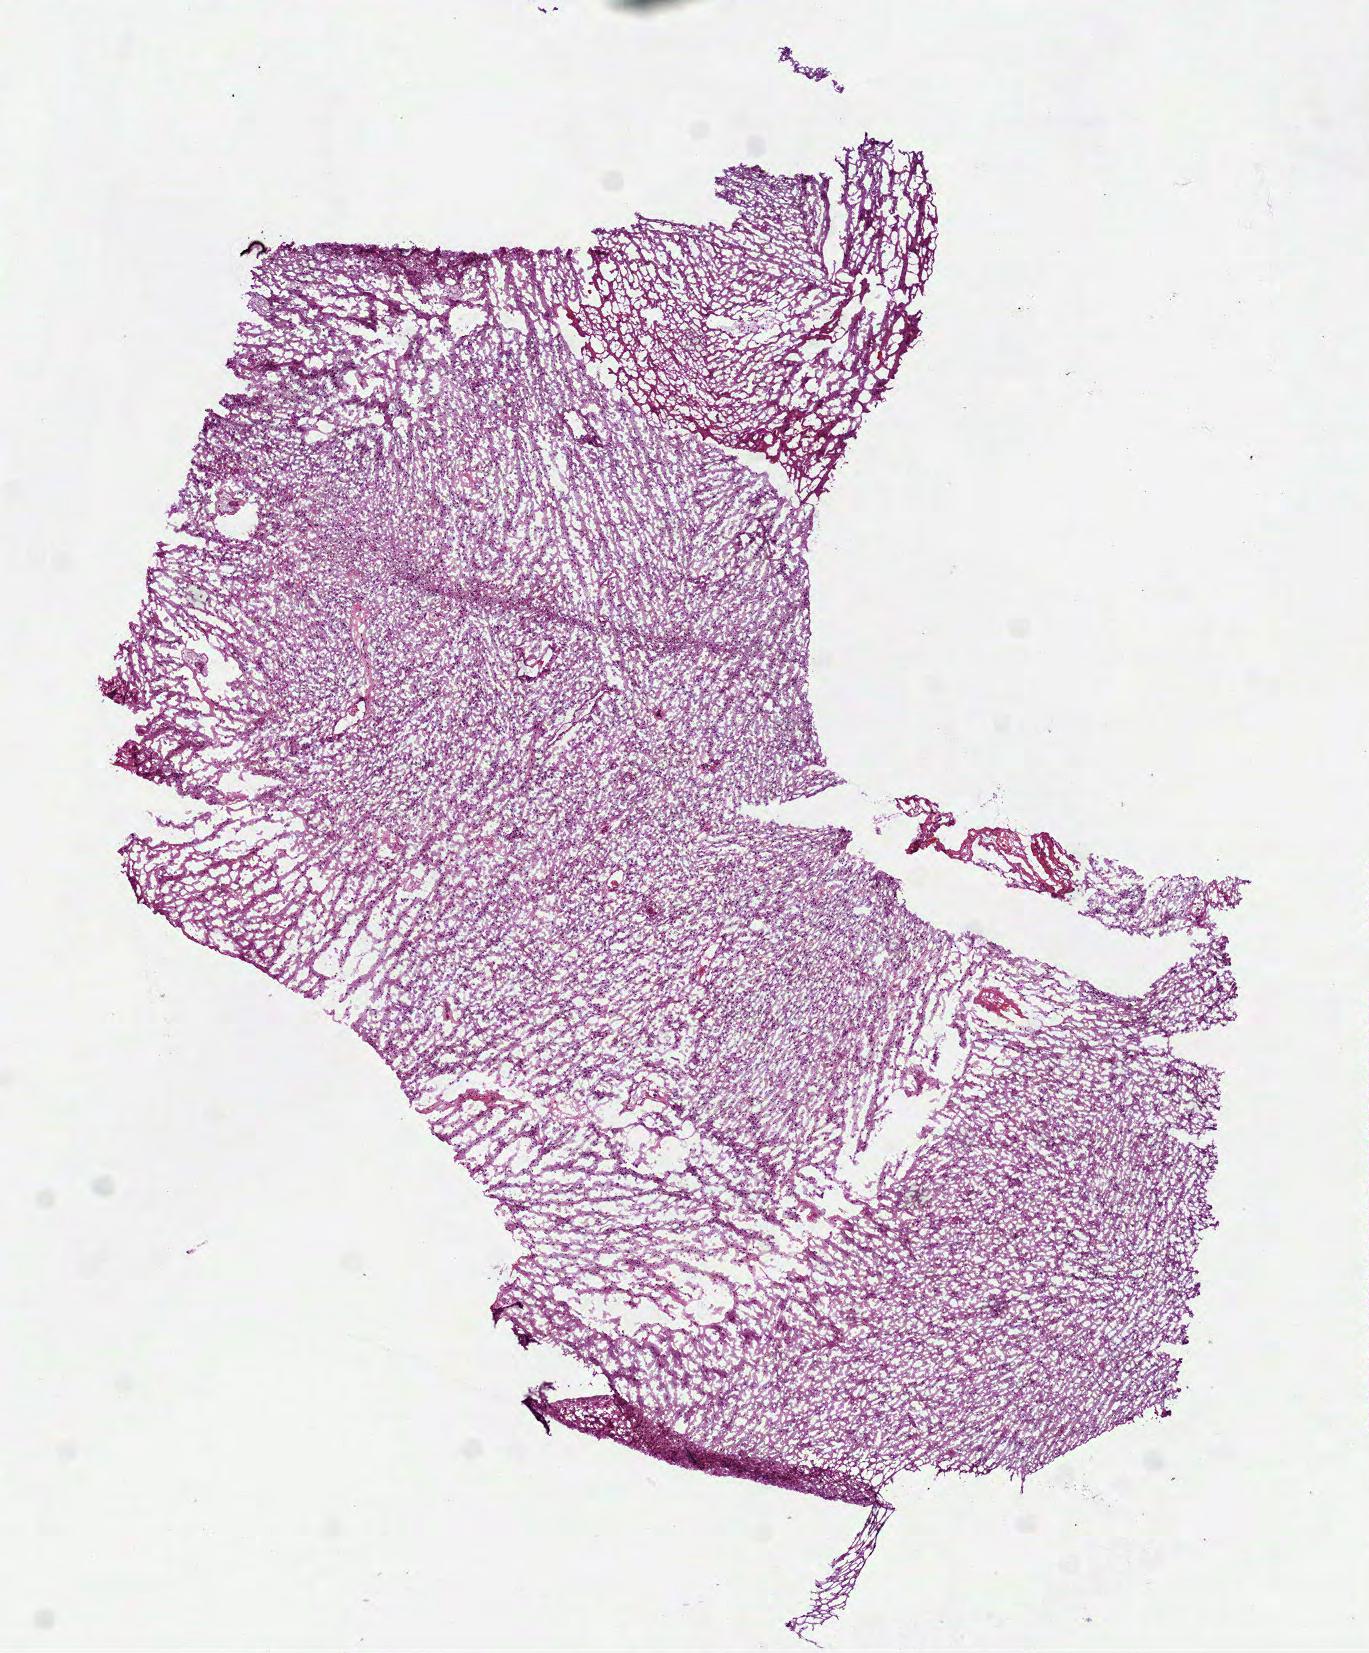
Digitized H&E-stained tissue section (whole slide) — a low-resolution overview of the entire scanned area, about 5.5 x 6.7 mm (acquisition: 40x scan), frozen section from the bottom of the tissue portion, primary tumour sample from the brain. Male, age 48 years at initial diagnosis. Histologic grade: G3 (poorly differentiated). Slide review estimates, as recorded: tumour cells 100%, tumour nuclei 70%, normal cells 0%, stromal cells 0%, necrosis 0%.
Pathologic diagnosis: Astrocytoma, anaplastic.